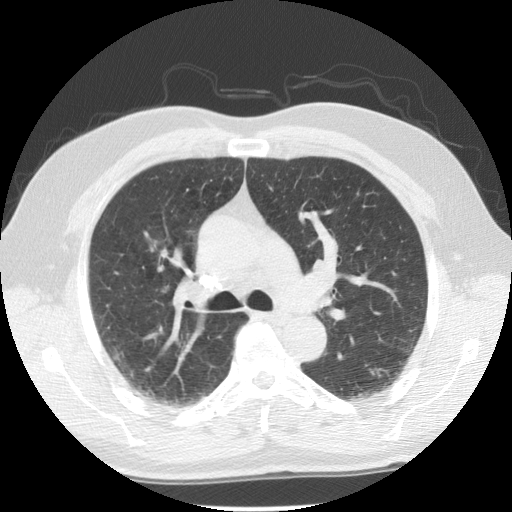
Low-dose screening chest CT, axial slice; baseline screening round; lung window (W 1500 / L -600 HU); 2.5 mm slice thickness; standard (soft-tissue) reconstruction kernel (STANDARD). Male, age 59 years at enrolment. Current smoker at enrolment.
• Expert-annotated lung lesion, box from (x=133, y=226) to (x=174, y=267) px.
• No non-calcified nodule or mass ≥4 mm was recorded by the screening reader at this exam.
• Official screen result: negative screen, minor abnormalities not suspicious for lung cancer.
• Later outcome: lung cancer diagnosed 659 days after this screen — large cell carcinoma, NOS, right upper lobe, poorly differentiated (G3), stage IIIA (AJCC 6th edition), 34 mm at pathology.